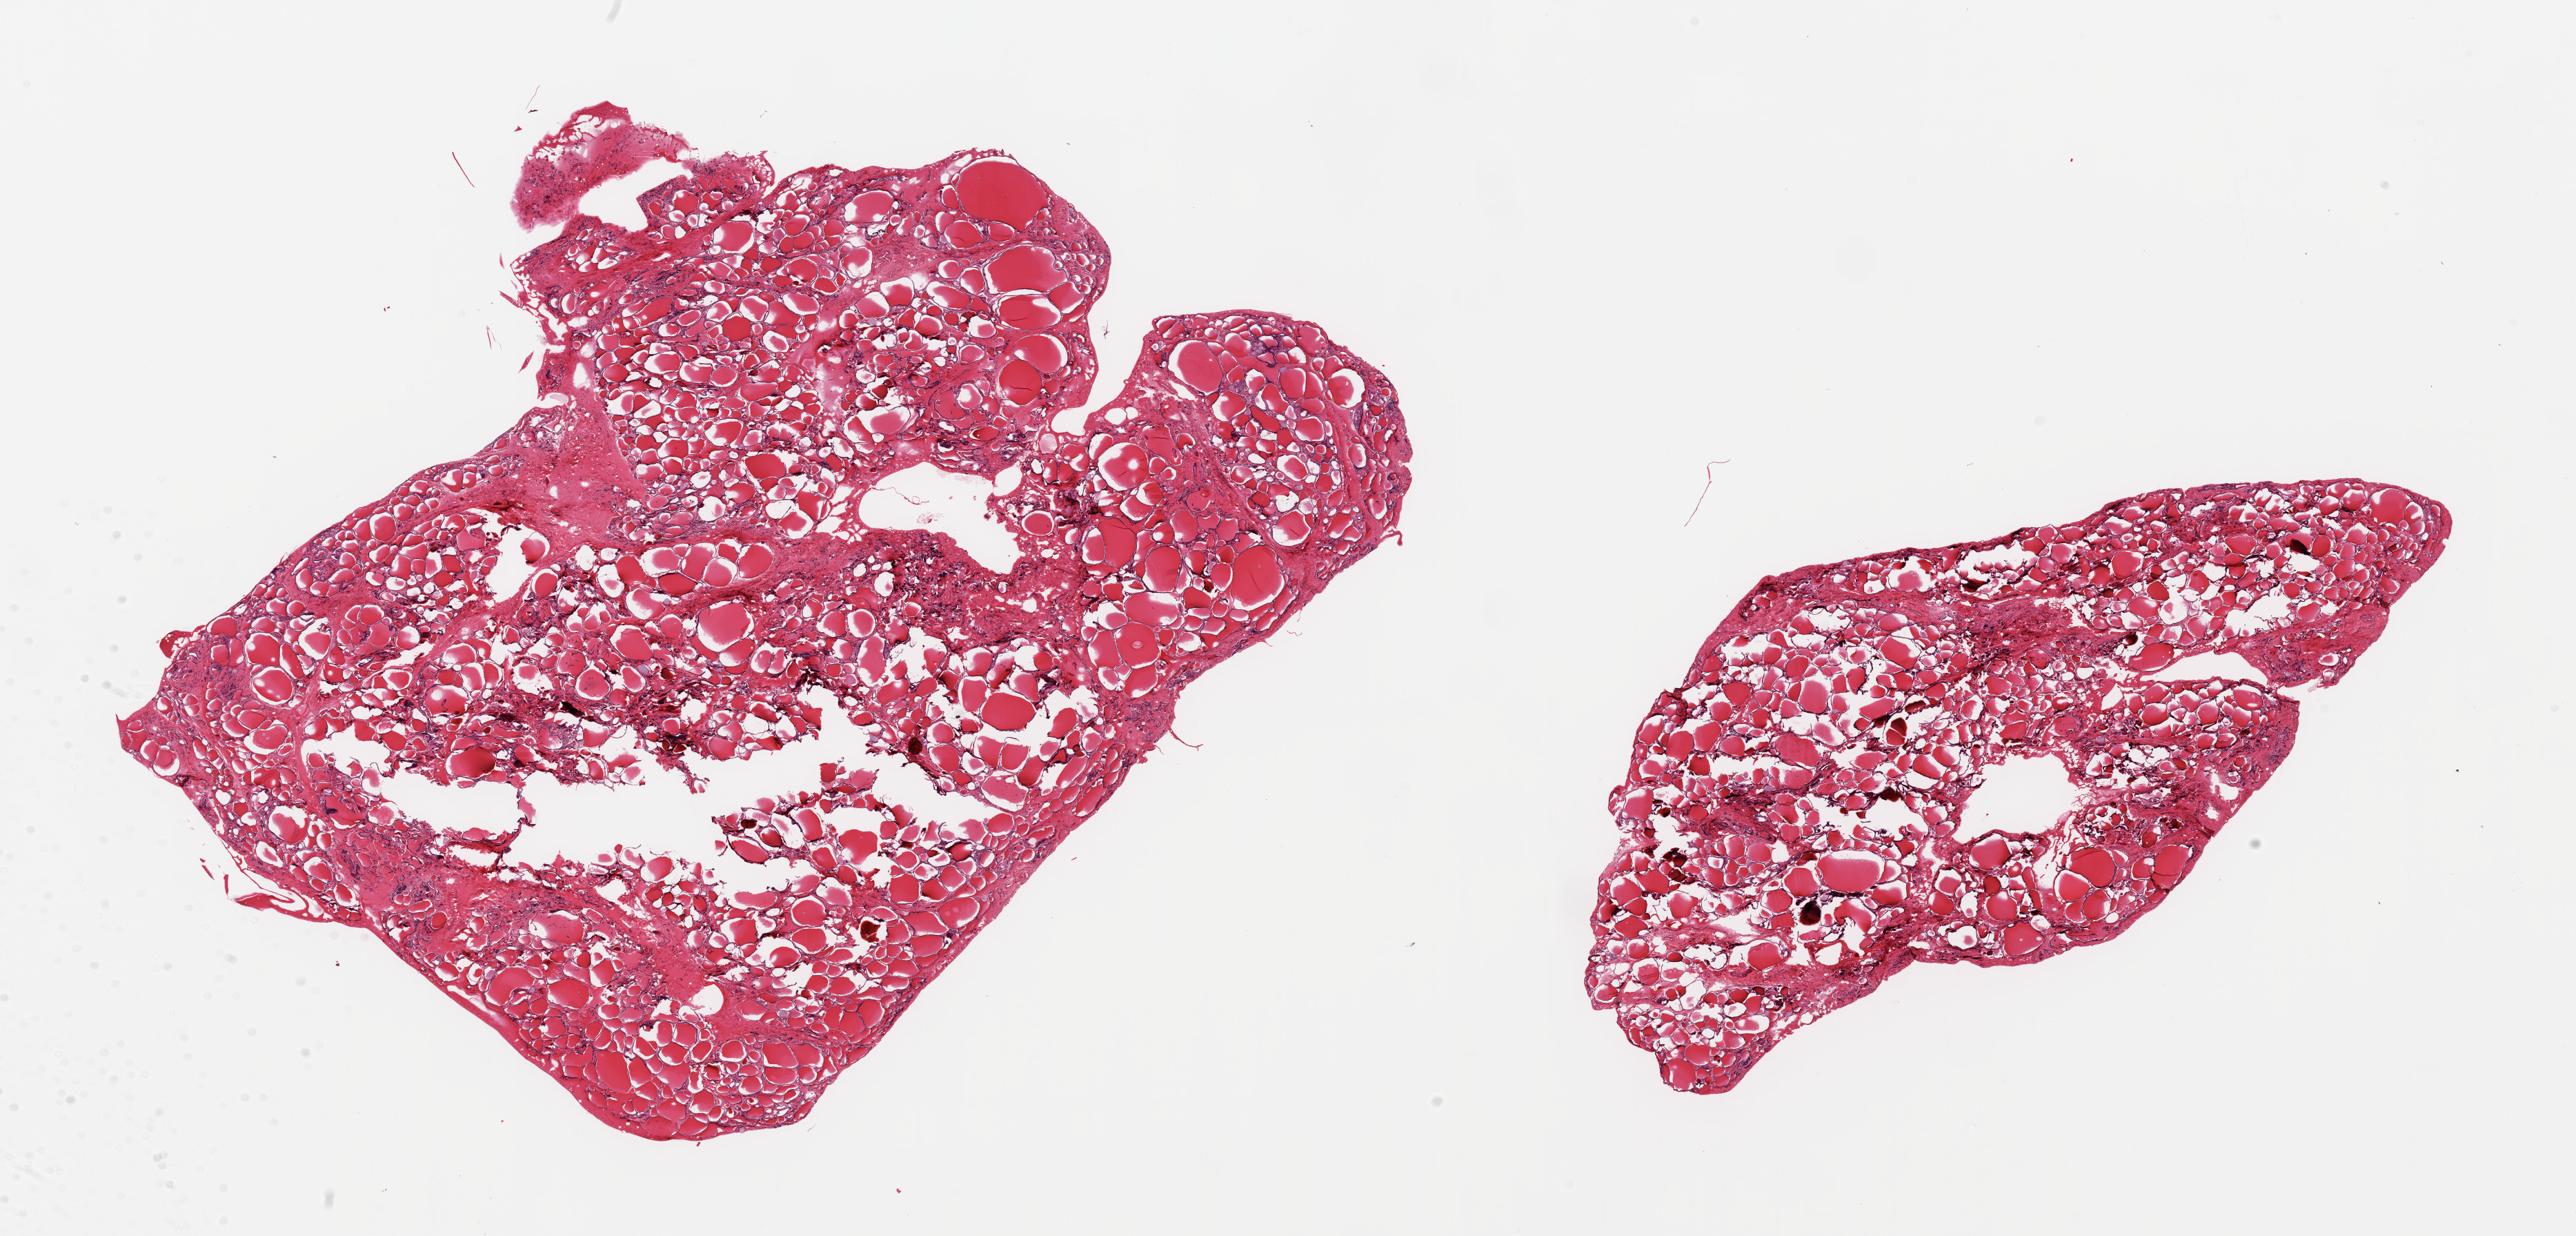
Digitized H&E-stained section, whole scanned area (about 29.5 x 14.2 mm, from a 20x scan) shown as a low-resolution overview. PAXgene-fixed, paraffin-embedded tissue. Section of thyroid (target tissue). Tissue donor sample. Male donor.
Review note (as recorded): 2 pieces; focally fragmented.